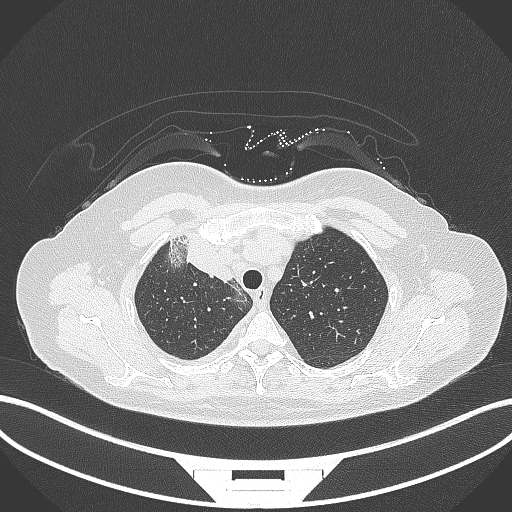
Chest CT, one axial slice; reconstruction kernel B70f; lung window (W 1500 / L -600 HU); 1 mm slice thickness; 512 × 512 image matrix. Patient: female, 52 years. From the clinical record (not read from this slice): clinical TNM (as recorded): T3 N1 M1.
Annotated regions visible in this slice (rectangle marked by the reading radiologist):
- lung tumour (recorded histology: adenocarcinoma): bounding box (x1, y1, x2, y2) in pixels: (170, 236, 236, 280)